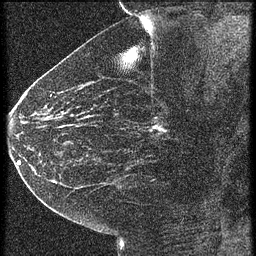
Breast MRI (dynamic contrast-enhanced), one sagittal slice; position 32 of 60 along the scan axis; 4 images stored at this slice position (order not interpretable as contrast timing); 1.5 T; TE 4.2 ms, TR 21.3 ms; 1.5 mm slice thickness; 256 × 256 image matrix, field of view 180 × 180 mm. Patient: female, 43 years. Case-level facts recorded for this patient, not image findings: setting: breast cancer imaged before/during neoadjuvant chemotherapy; receptor status: HER2-positive.
Annotated regions visible in this slice (semi-automatic segmentation, software-assisted and operator-edited):
- analysis volume of interest (the breast-tissue region the enhancement analysis was run in; not a lesion): bounding box [x1, y1, x2, y2] px = [122, 100, 187, 151]
- tumour enhancement mask (voxels above the 90 % enhancement threshold inside the analysis volume of interest): [154, 118, 165, 131]